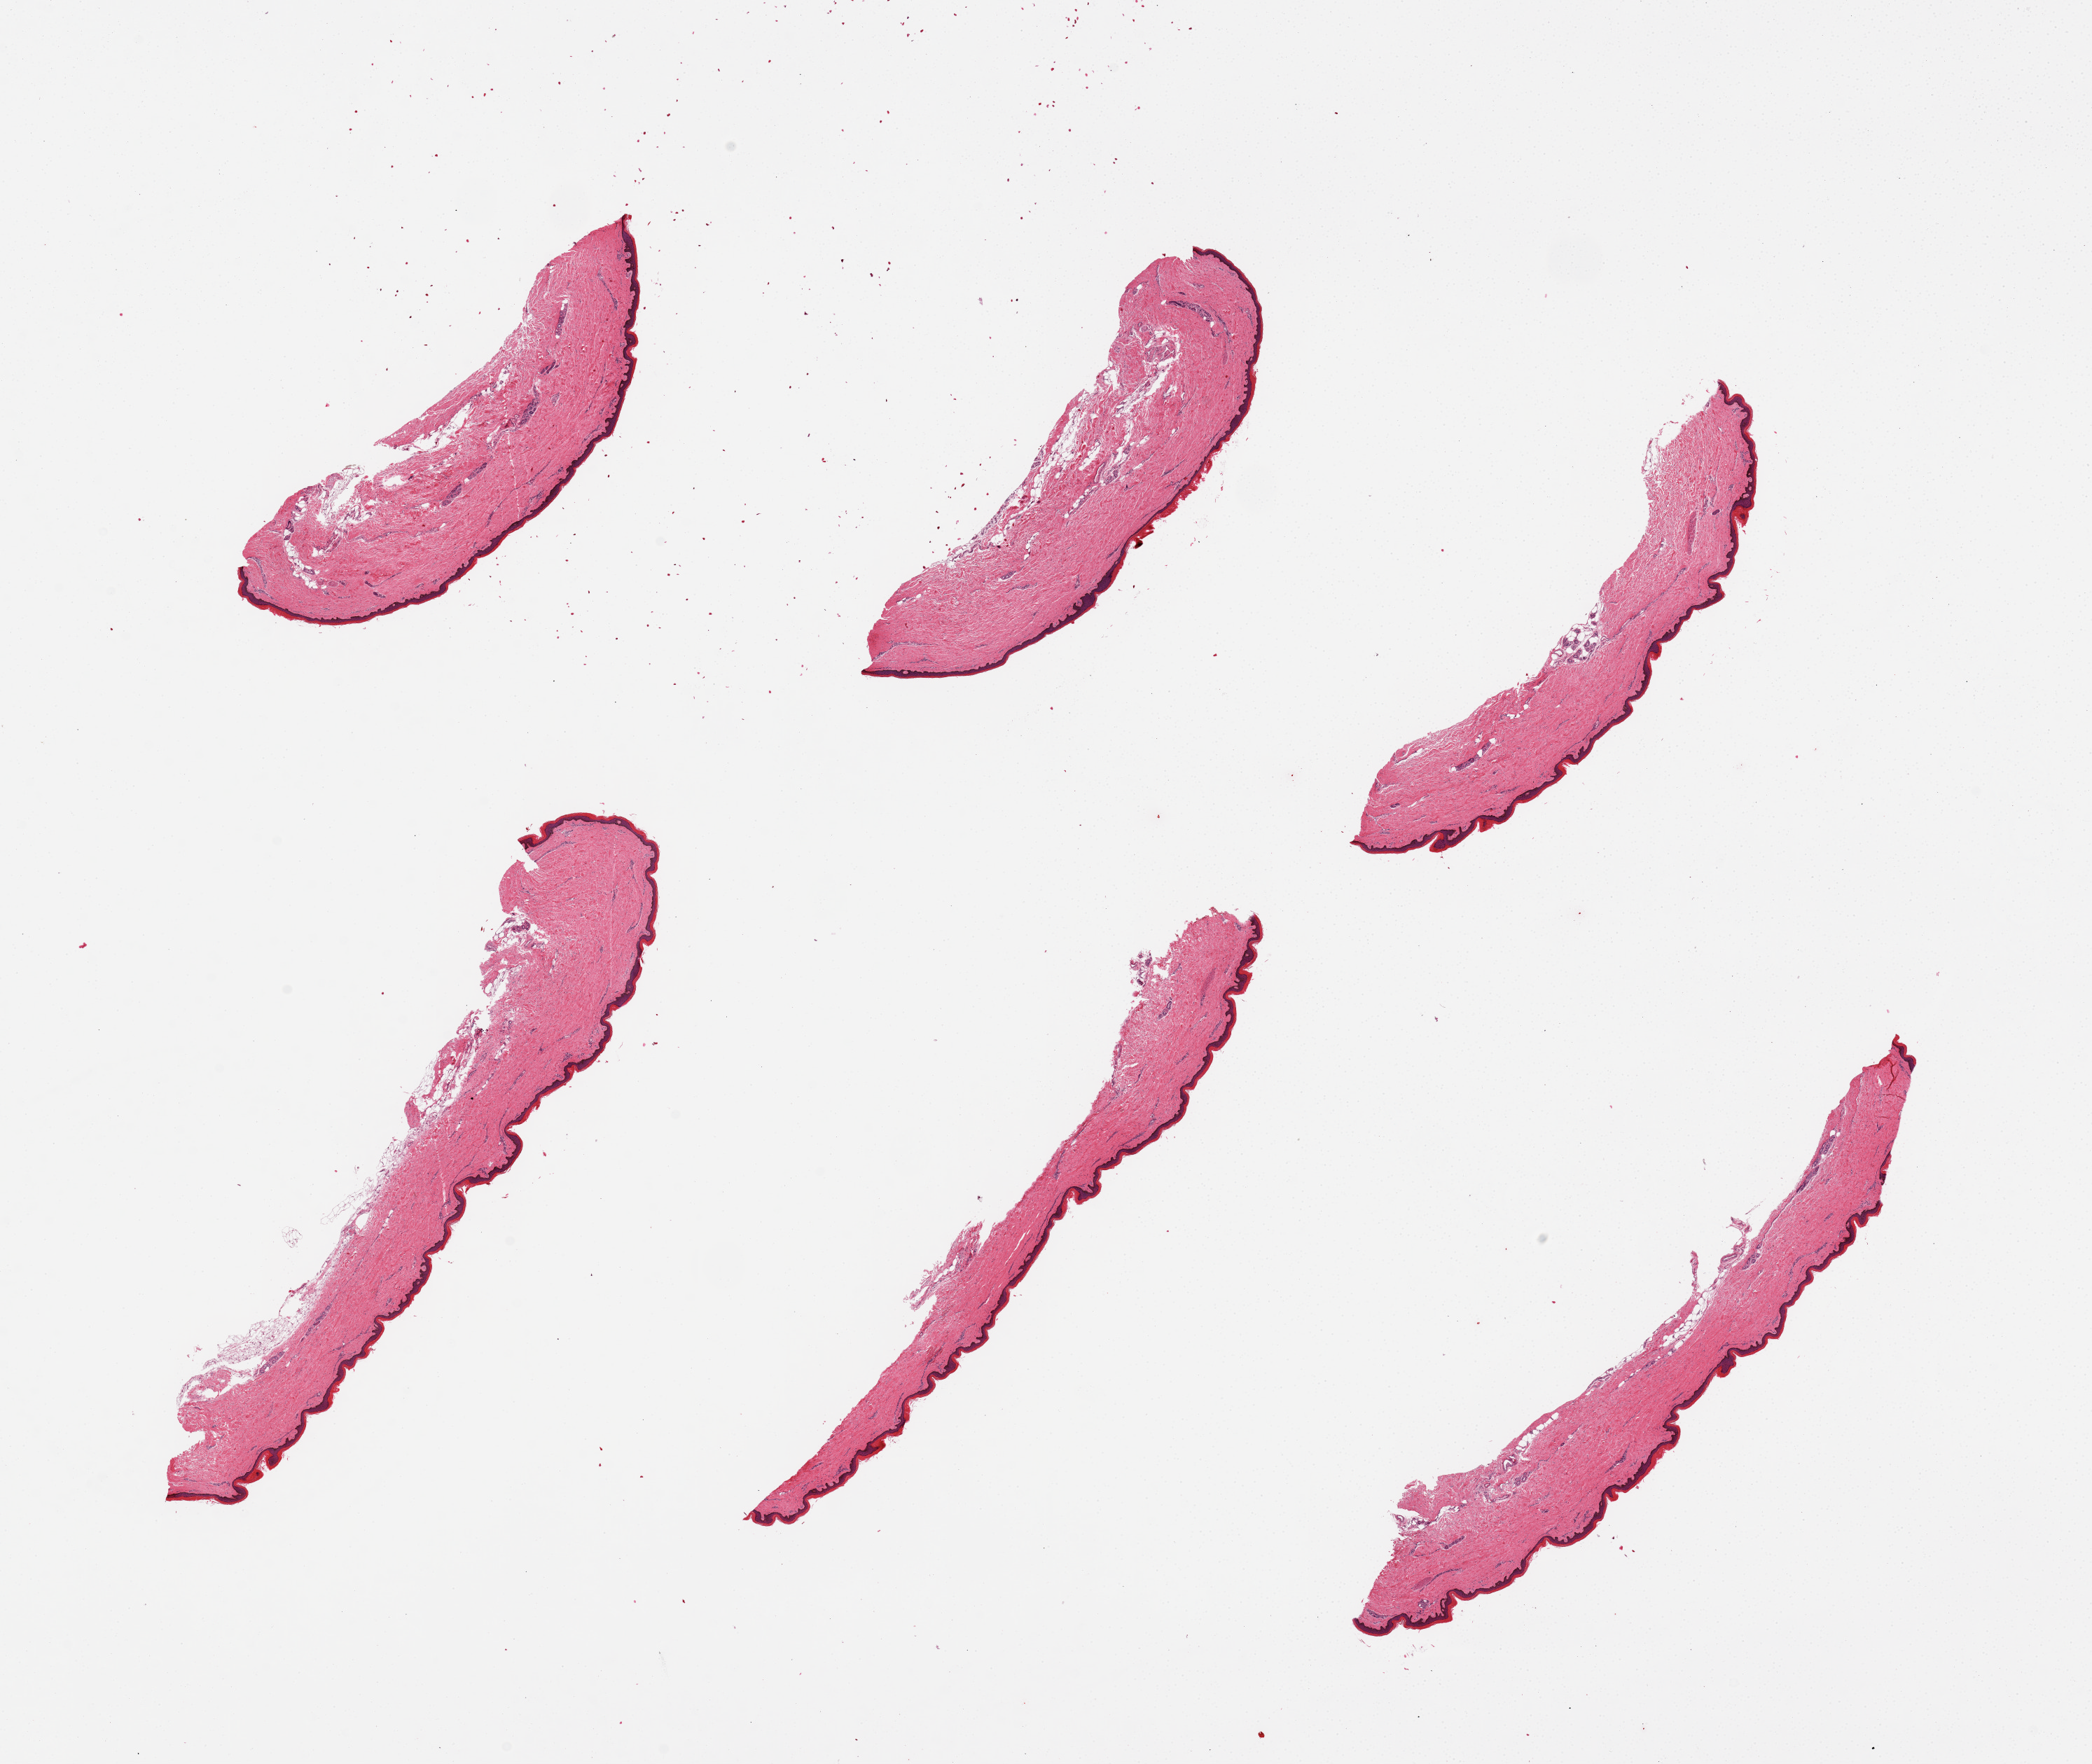
Whole-slide image, H&E stain, brightfield, shown as a low-resolution overview of the whole scanned area (about 23.6 x 19.9 mm, from a 20x scan); PAXgene-fixed, paraffin-embedded tissue; sampled site (target tissue): skin of lower leg; donor tissue sample. Donor: female.
* pathologist's review note for this sample: 6 pieces. Squamous epithelium is ~3% of thickness. Minimal dermal fat